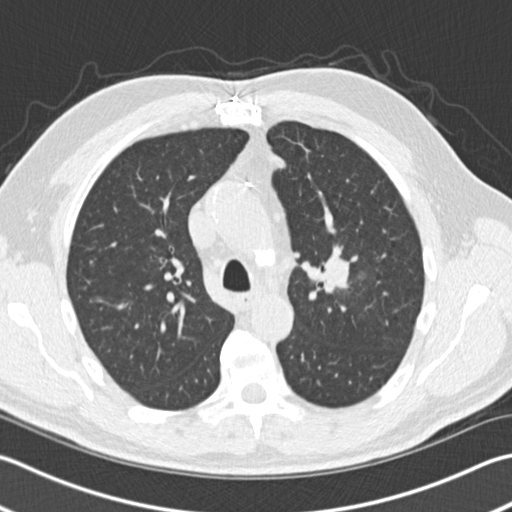
Chest CT (low-dose screening protocol), one axial image; third annual screen; lung window (W 1500 / L -600 HU); 2 mm slice thickness; standard (soft-tissue) reconstruction kernel (B30f); 120 kVp; slice 49 of 153 in the series; 512 × 512 image matrix. Male participant, aged 65 years at enrolment. Former smoker at enrolment.
• Expert reader's lesion annotation, bounding box [x1, y1, x2, y2] px = [307, 239, 371, 303].
• The screening reader recorded 4 non-calcified nodules or masses ≥4 mm on this exam (left upper lobe, left upper lobe, left lower lobe, right middle lobe); which of them this box marks is not recorded.
• Later outcome: lung cancer diagnosed 196 days after this screen — acinar cell carcinoma, left upper lobe, stage IA (AJCC 6th edition), 25 mm at pathology.